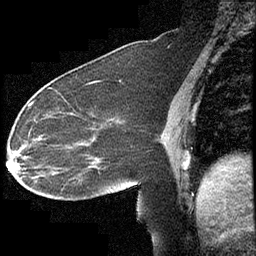
Breast MRI (dynamic contrast-enhanced), one sagittal slice. Position 159 of 232 along the scan axis. Dynamic contrast-enhanced study with each time point stored as its own series, time point 2 of 4 at this slice position (early post-contrast, ordered by acquisition time). 1.5 T. TE 4.2 ms, TR 6.7 ms. 3 mm slice thickness. 256 × 256 image matrix. Female patient, age 63 years. Case-level facts recorded for this patient, not image findings: setting: breast cancer imaged before/during neoadjuvant chemotherapy; receptor status: triple-negative.
Structures marked on this image (semi-automatically segmented with operator editing):
- analysis volume of interest (the breast-tissue region the enhancement analysis was run in; not a lesion): box from (x=13, y=90) to (x=140, y=211) px
- tumour enhancement mask (voxels above the 70 % enhancement threshold inside the analysis volume of interest): (x=14, y=102)–(x=33, y=157)